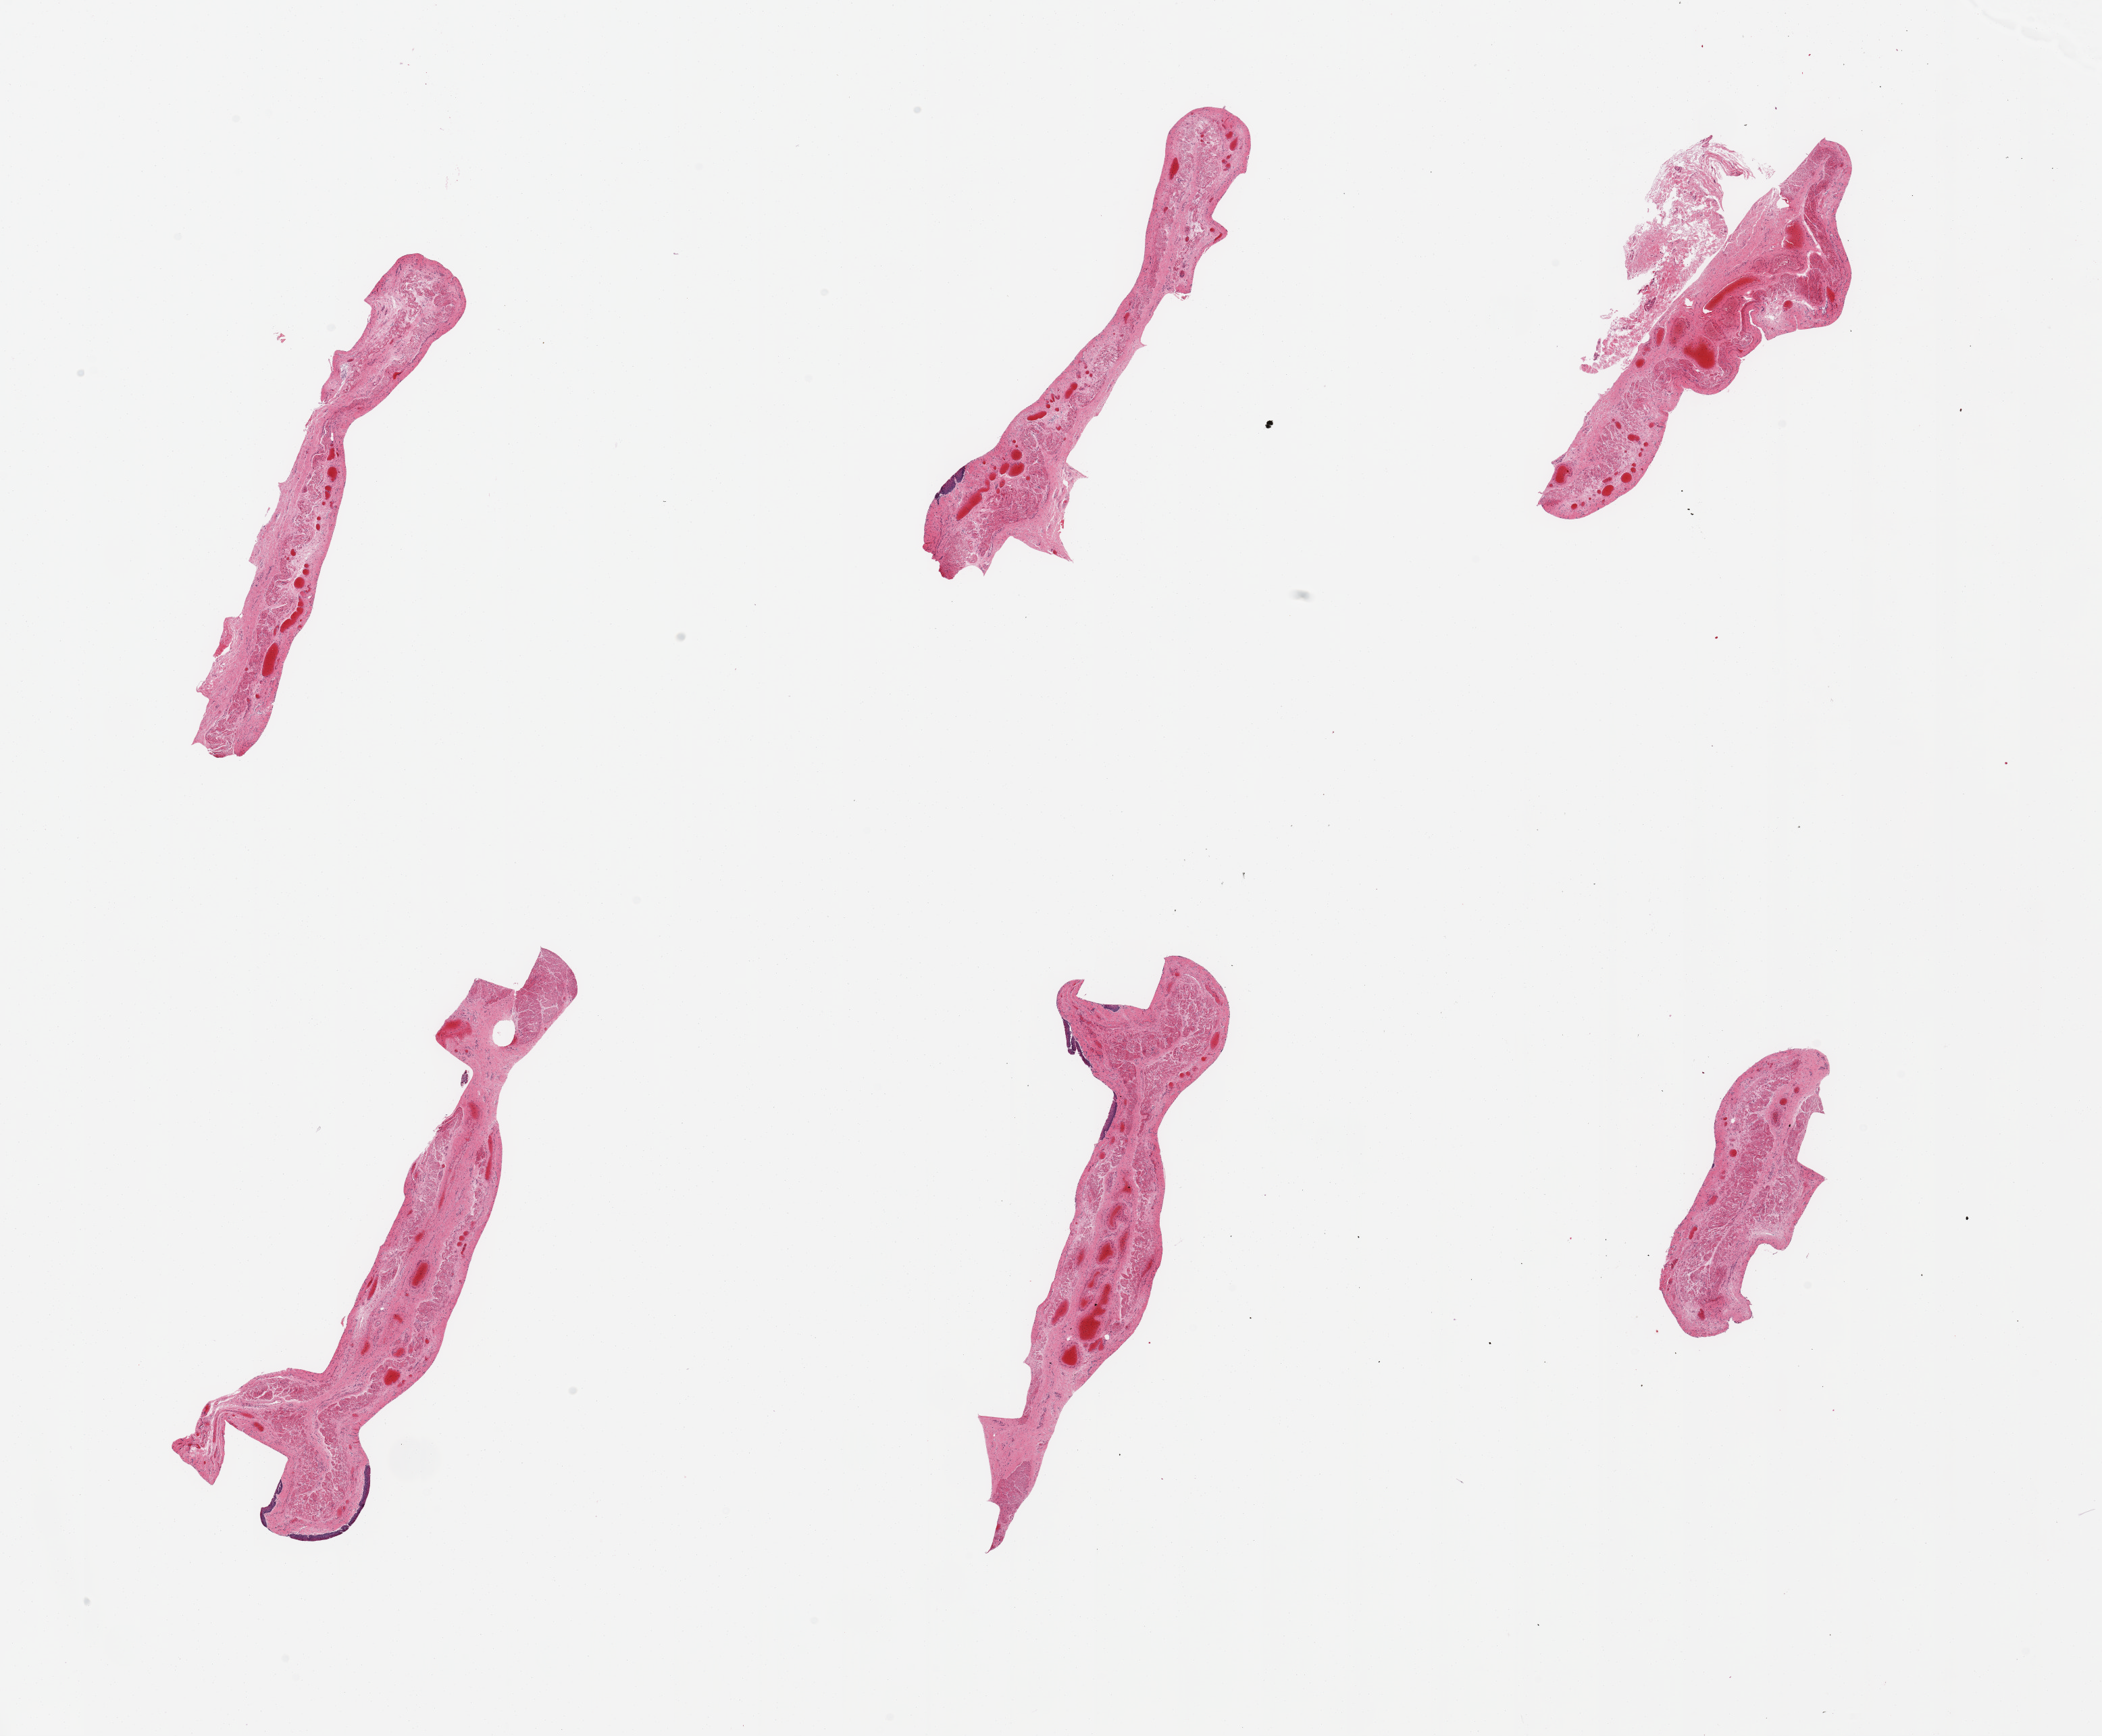
Digitized H&E-stained section, brightfield, low-resolution overview of the scanned area, about 24.6 x 20.3 mm. PAXgene-fixed paraffin-embedded (PFPE) section. Sampled site (target tissue): esophageal mucous membrane. Tissue donor sample.
Review note (as recorded): 6 pieces, target mucosa largely sloughed, trace residual up to ~50 microns.